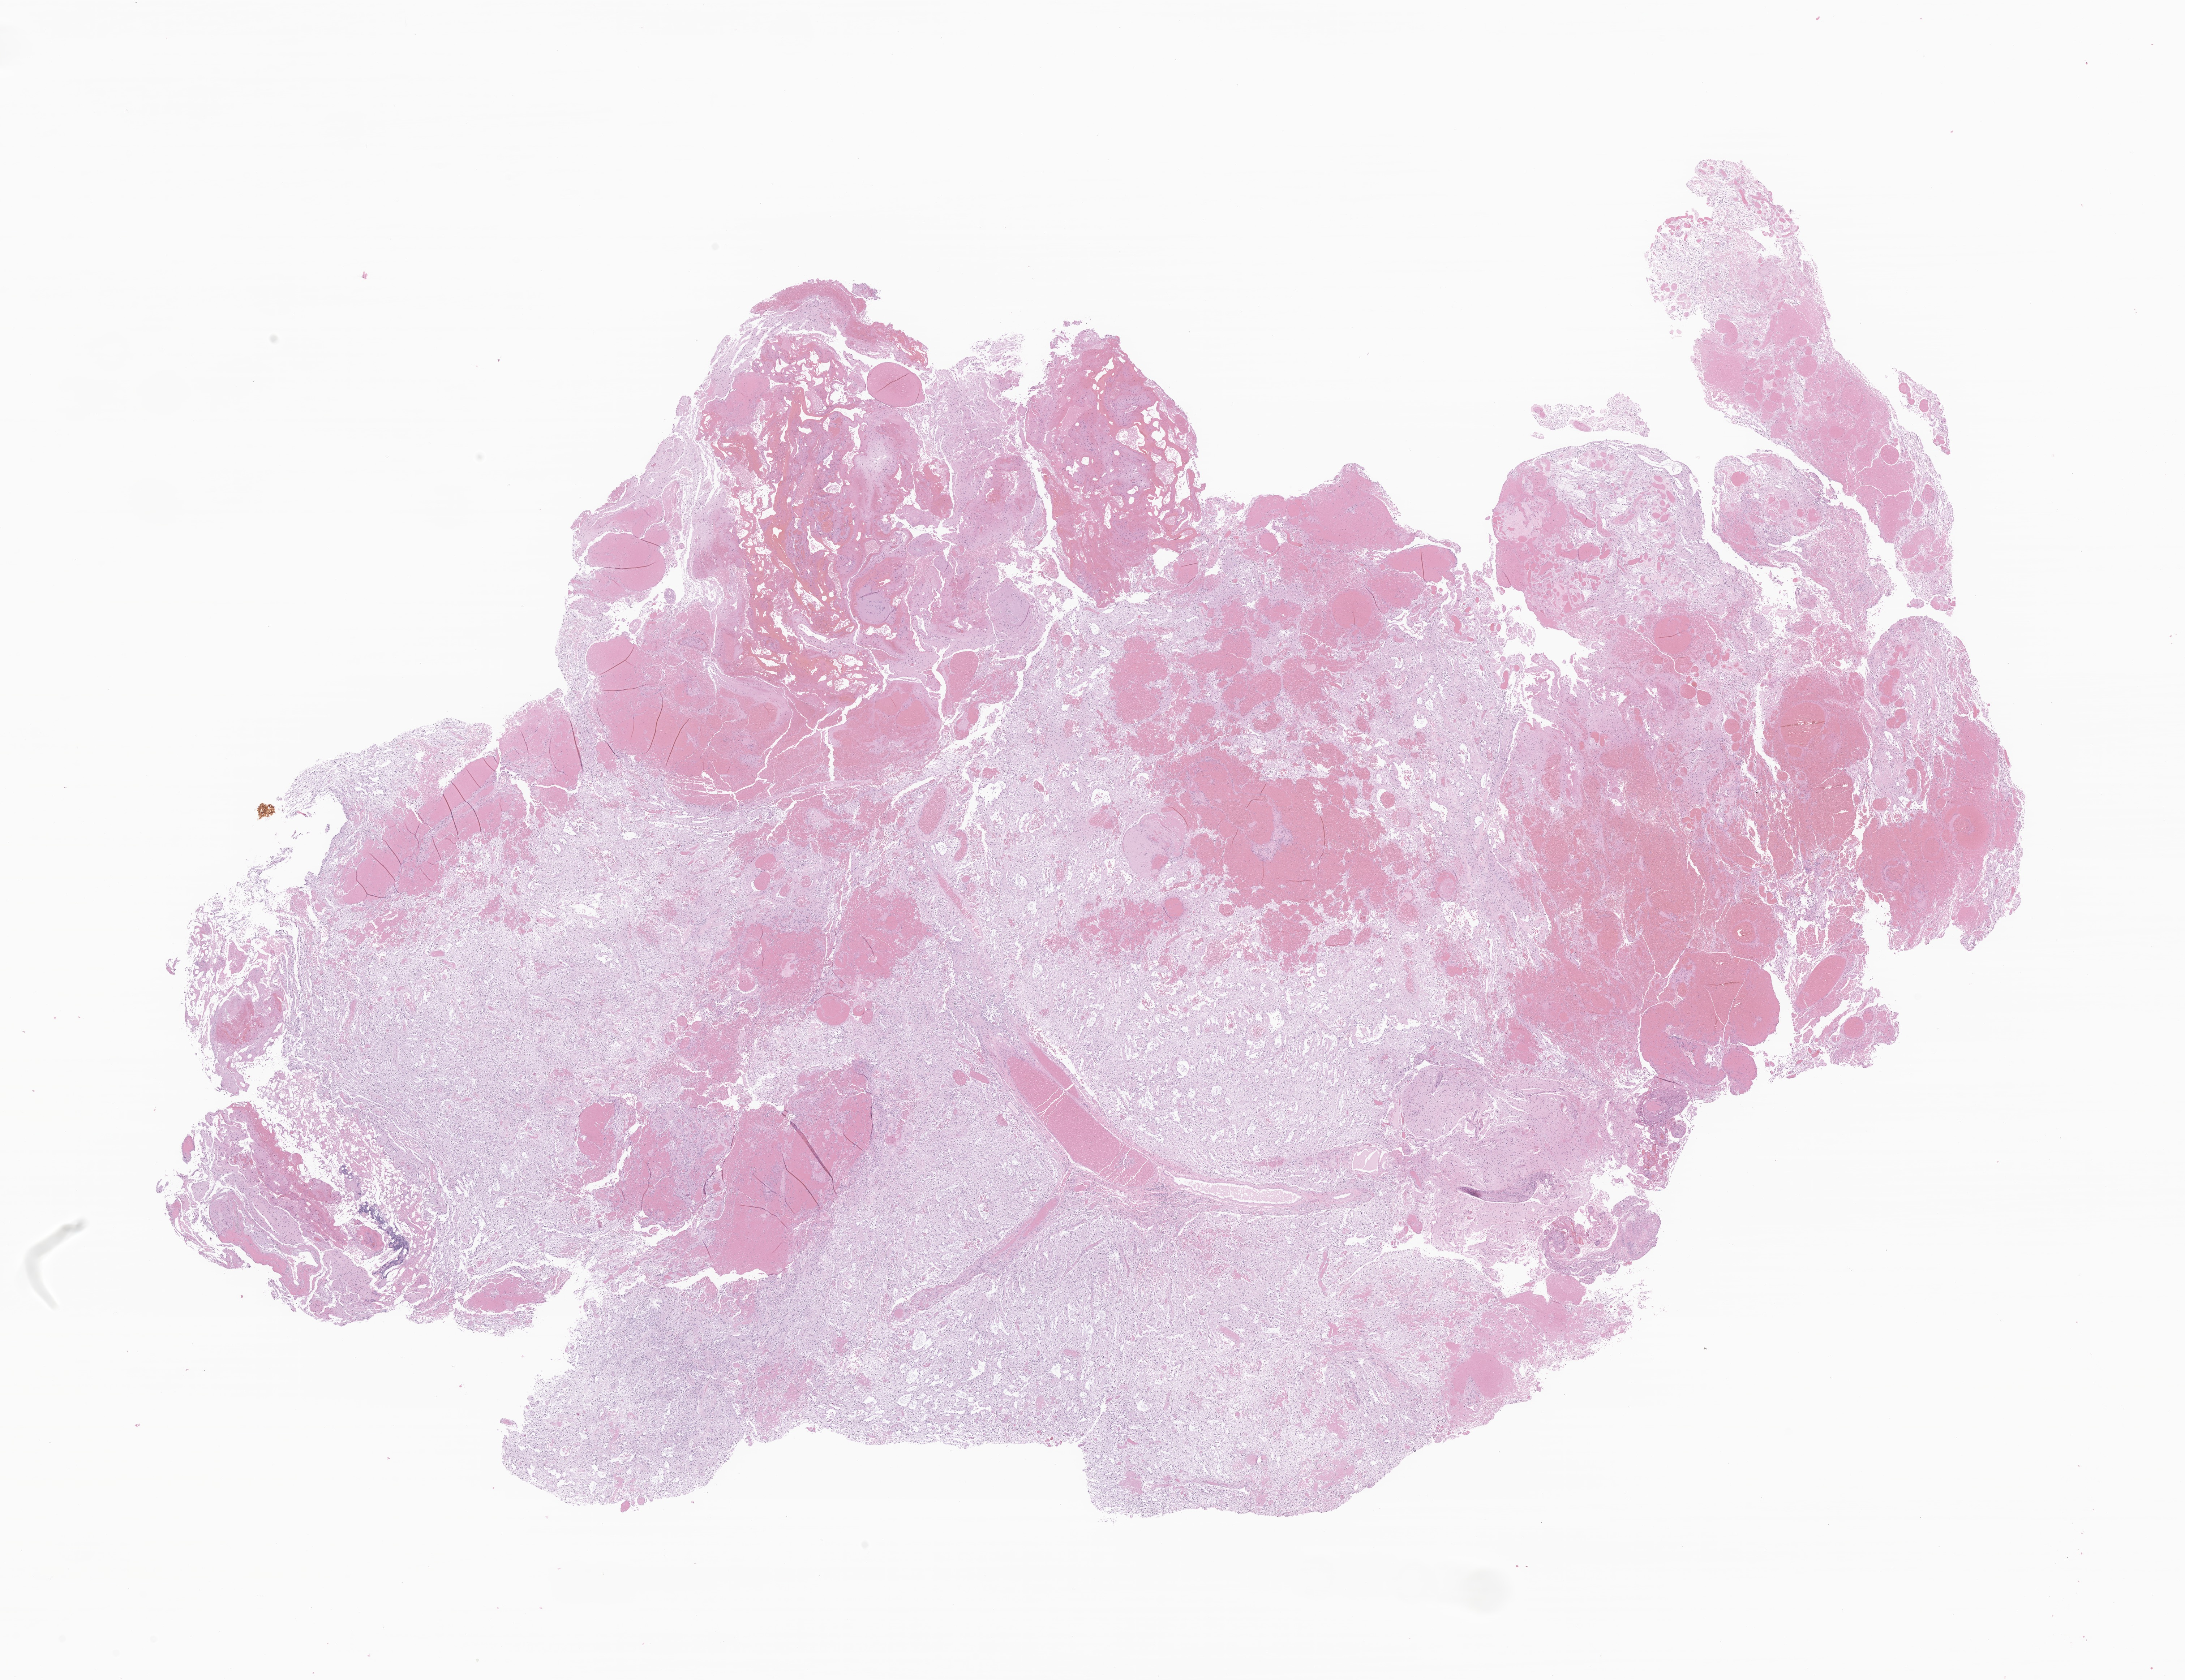
Whole-slide image, H&E stain of tumor tissue from the central nervous system, low-resolution overview of the scanned area, about 25.5 x 19.6 mm. Formalin-fixed paraffin-embedded section. Patient: female, age 186 months.
Diagnosis: Medulloblastoma, NOS.